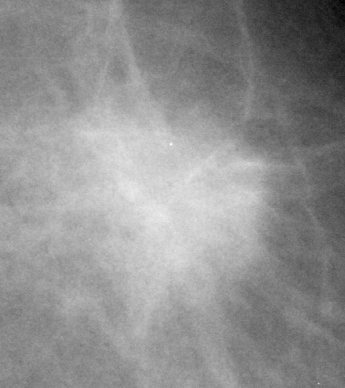
Crop from a digitized film mammogram around one marked abnormality; left breast; CC view; BI-RADS breast density category 1 (scale 1–4).
Finding: mass, shape irregular, margins spiculated; BI-RADS assessment category 5; pathology (as recorded): malignant.